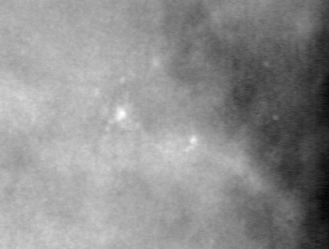
Region of interest cut from a scanned film mammogram (one marked finding); right breast; MLO view.
Finding: calcifications, morphology pleomorphic, distribution clustered; BI-RADS assessment category 4; subtlety rating 3 on a 1 (subtle) to 5 (obvious) scale; pathology result (as recorded, not read from the image): malignant.